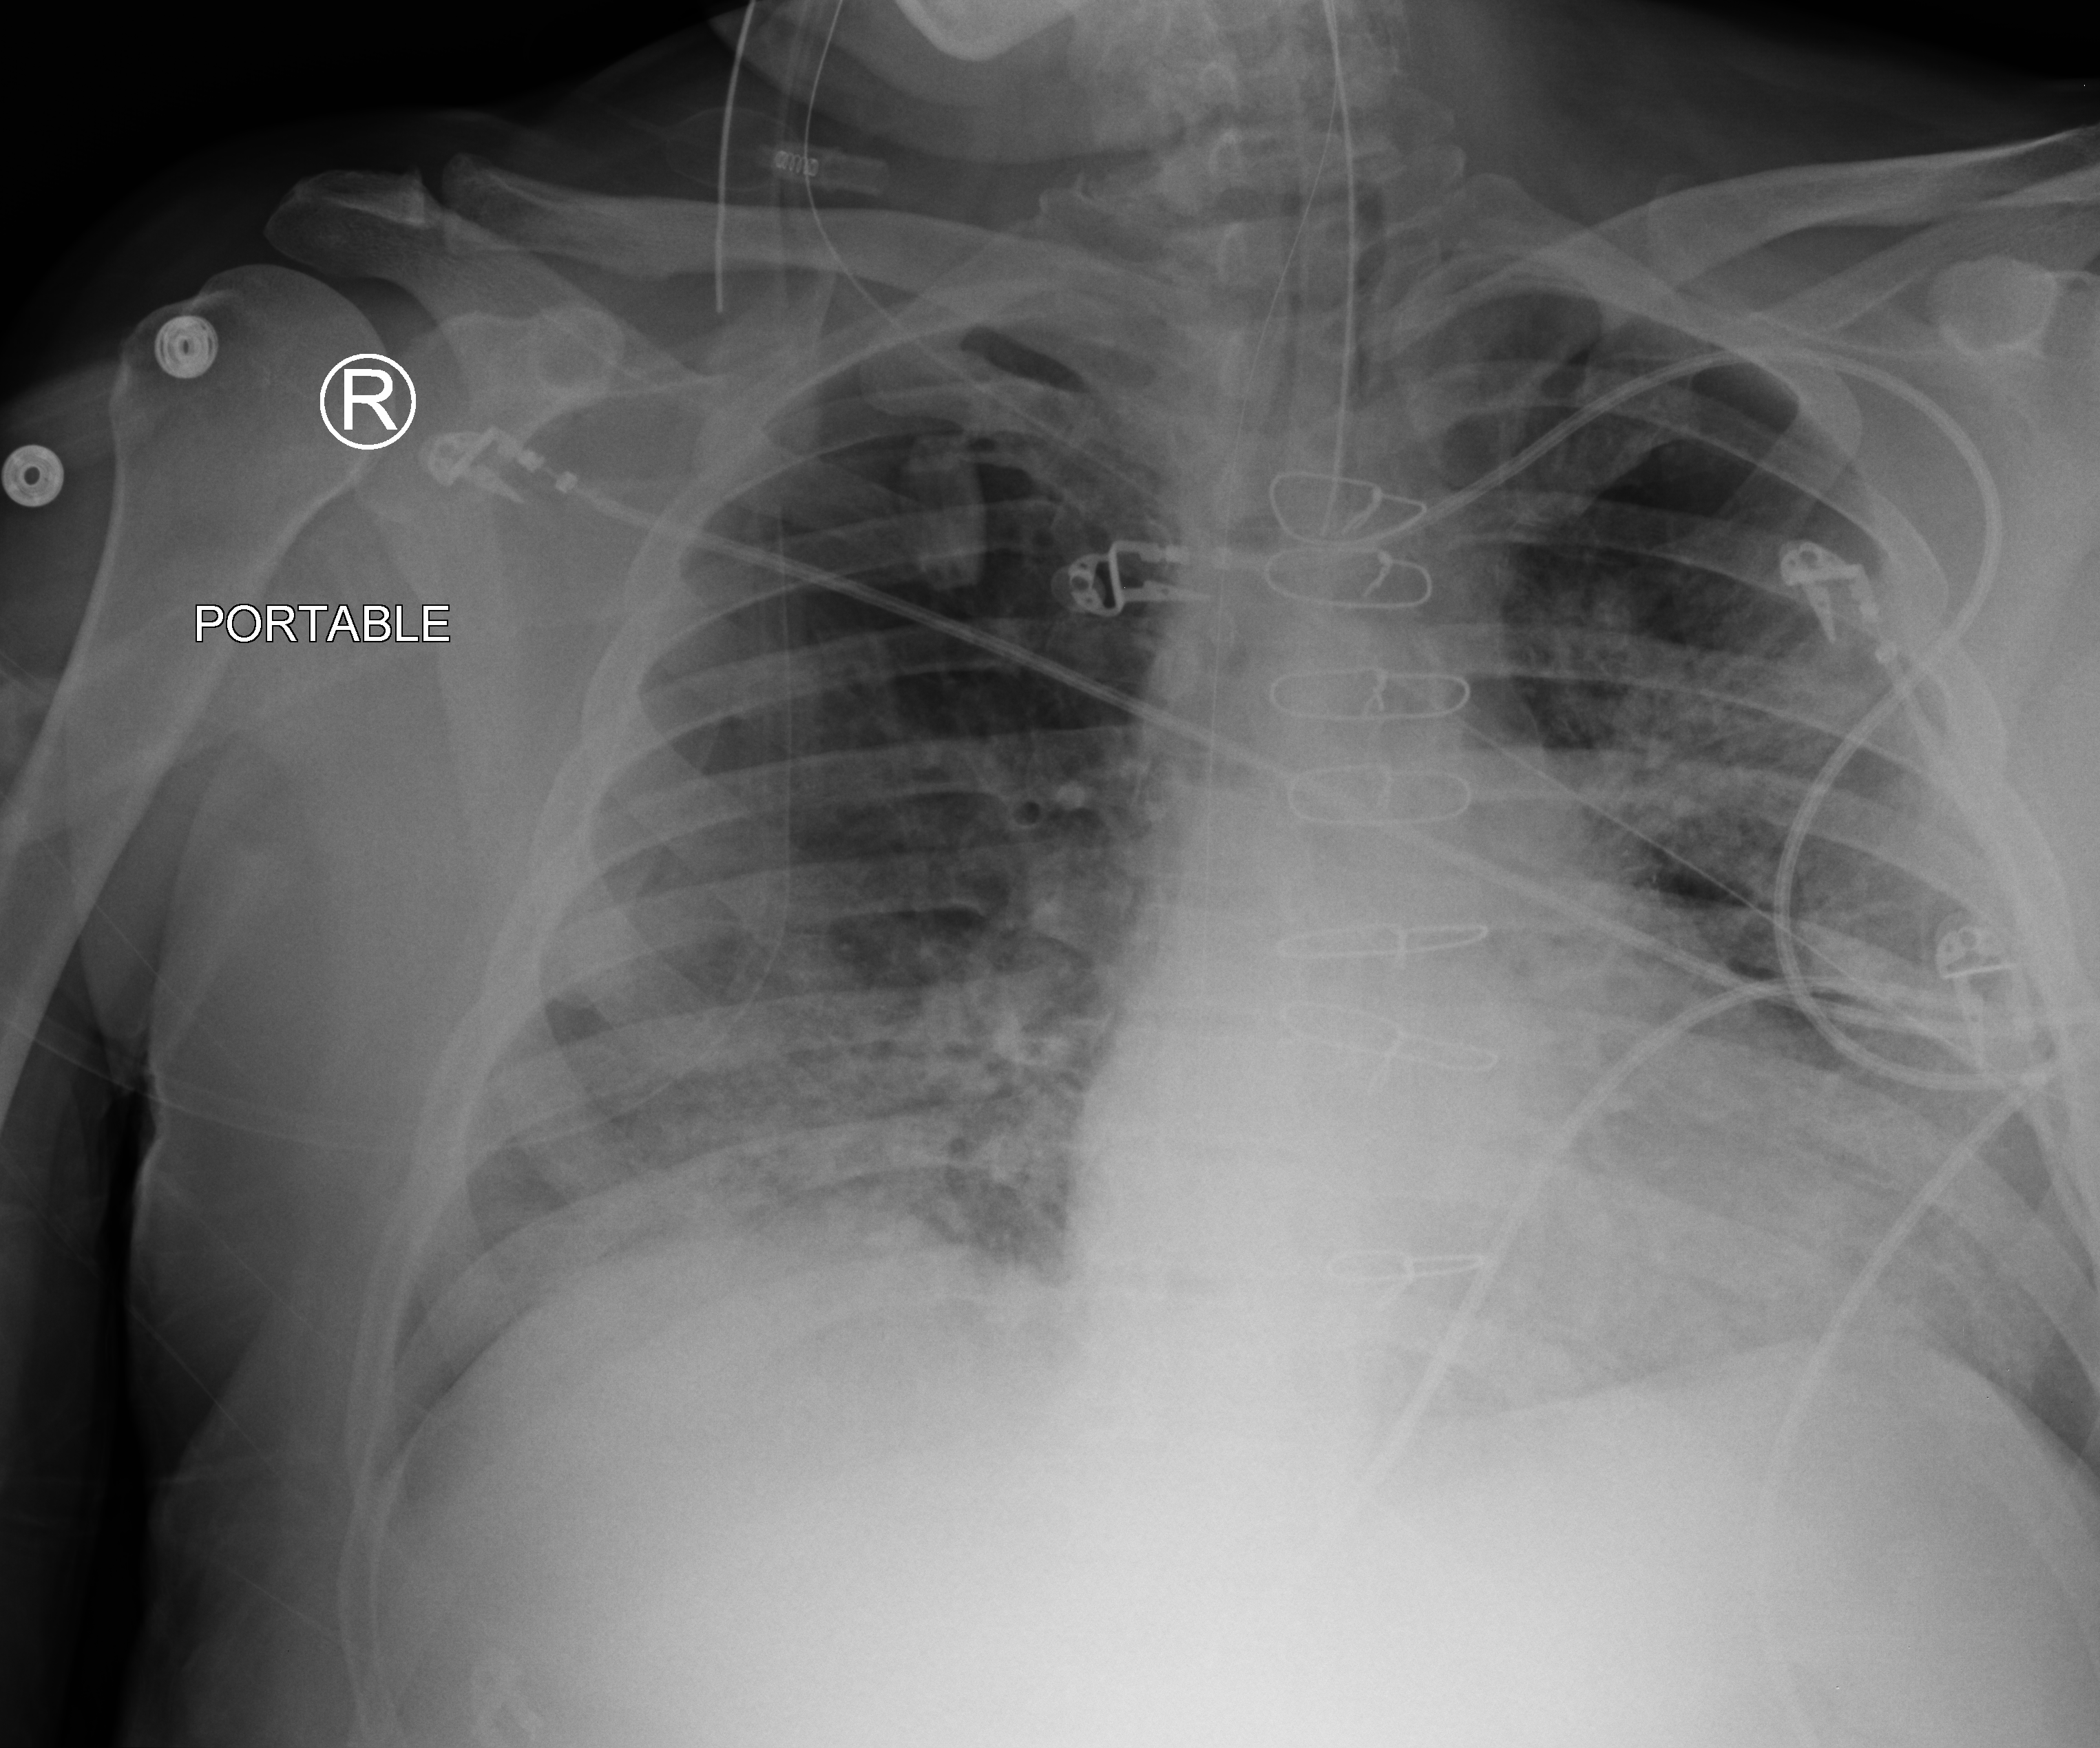
Portable chest radiograph, anteroposterior (AP) projection. Patient hospitalised with COVID-19; male, aged 60–74 years.
From the hospital-stay record, not from the radiograph (when in the stay this image was taken is not recorded):
- diabetes (admission record): yes